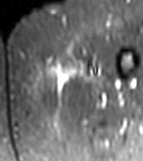
MRI of an extremity soft-tissue mass, one axial slice; position 3 of 81 along the scan axis; STIR; MR volume resampled by the dataset authors to the PET/CT grid (not the native acquisition matrix); 143 × 161 image matrix, field of view 140 × 157 mm. Female patient. Case-level facts recorded for this patient, not image findings: histological type: myxofibrosarcoma; grade: intermediate; site of the primary tumour: left thigh.
Structures marked on this image (expert contour drawn on MRI and transferred to this co-registered scan by the dataset authors):
- gross tumour volume including surrounding oedema: bounding box (x1, y1, x2, y2) in pixels: (49, 62, 107, 89)